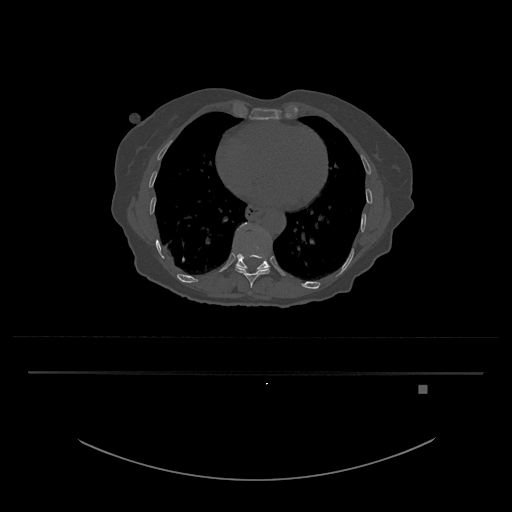
CT including the spine, one axial slice. Slice 696 of 797 in the series (ordered by position). Reconstruction kernel Br40s/3. Bone window (W 1800 / L 400 HU). 0.5 mm slice thickness. 512 × 512 image matrix, field of view 500 × 500 mm. Female patient, age 57 years. Case-level facts recorded for this patient, not image findings: primary cancer: cervical.
Annotated regions visible in this slice (semi-automatically segmented with operator editing):
- T10 vertebra: box from (x=235, y=255) to (x=270, y=288) px
- T11 vertebra: (x=233, y=222)–(x=270, y=270)